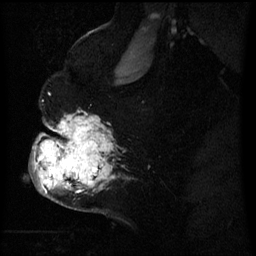
Breast MRI (dynamic contrast-enhanced), one sagittal slice; position 42 of 60 along the scan axis; dynamic contrast-enhanced series, image 2 of 3 at this slice position (ordered by acquisition); 1.5 T; TE 4.2 ms, TR 8 ms; 256 × 256 image matrix. Patient: female, 50 years.
Annotated regions visible in this slice (semi-automatically segmented with operator editing):
- analysis volume of interest (the breast-tissue region the enhancement analysis was run in; not a lesion): bounding box <32,120,110,201> (left, top, right, bottom; pixels)
- tumour enhancement mask (voxels above the 70 % enhancement threshold inside the analysis volume of interest): <35,120,105,185>